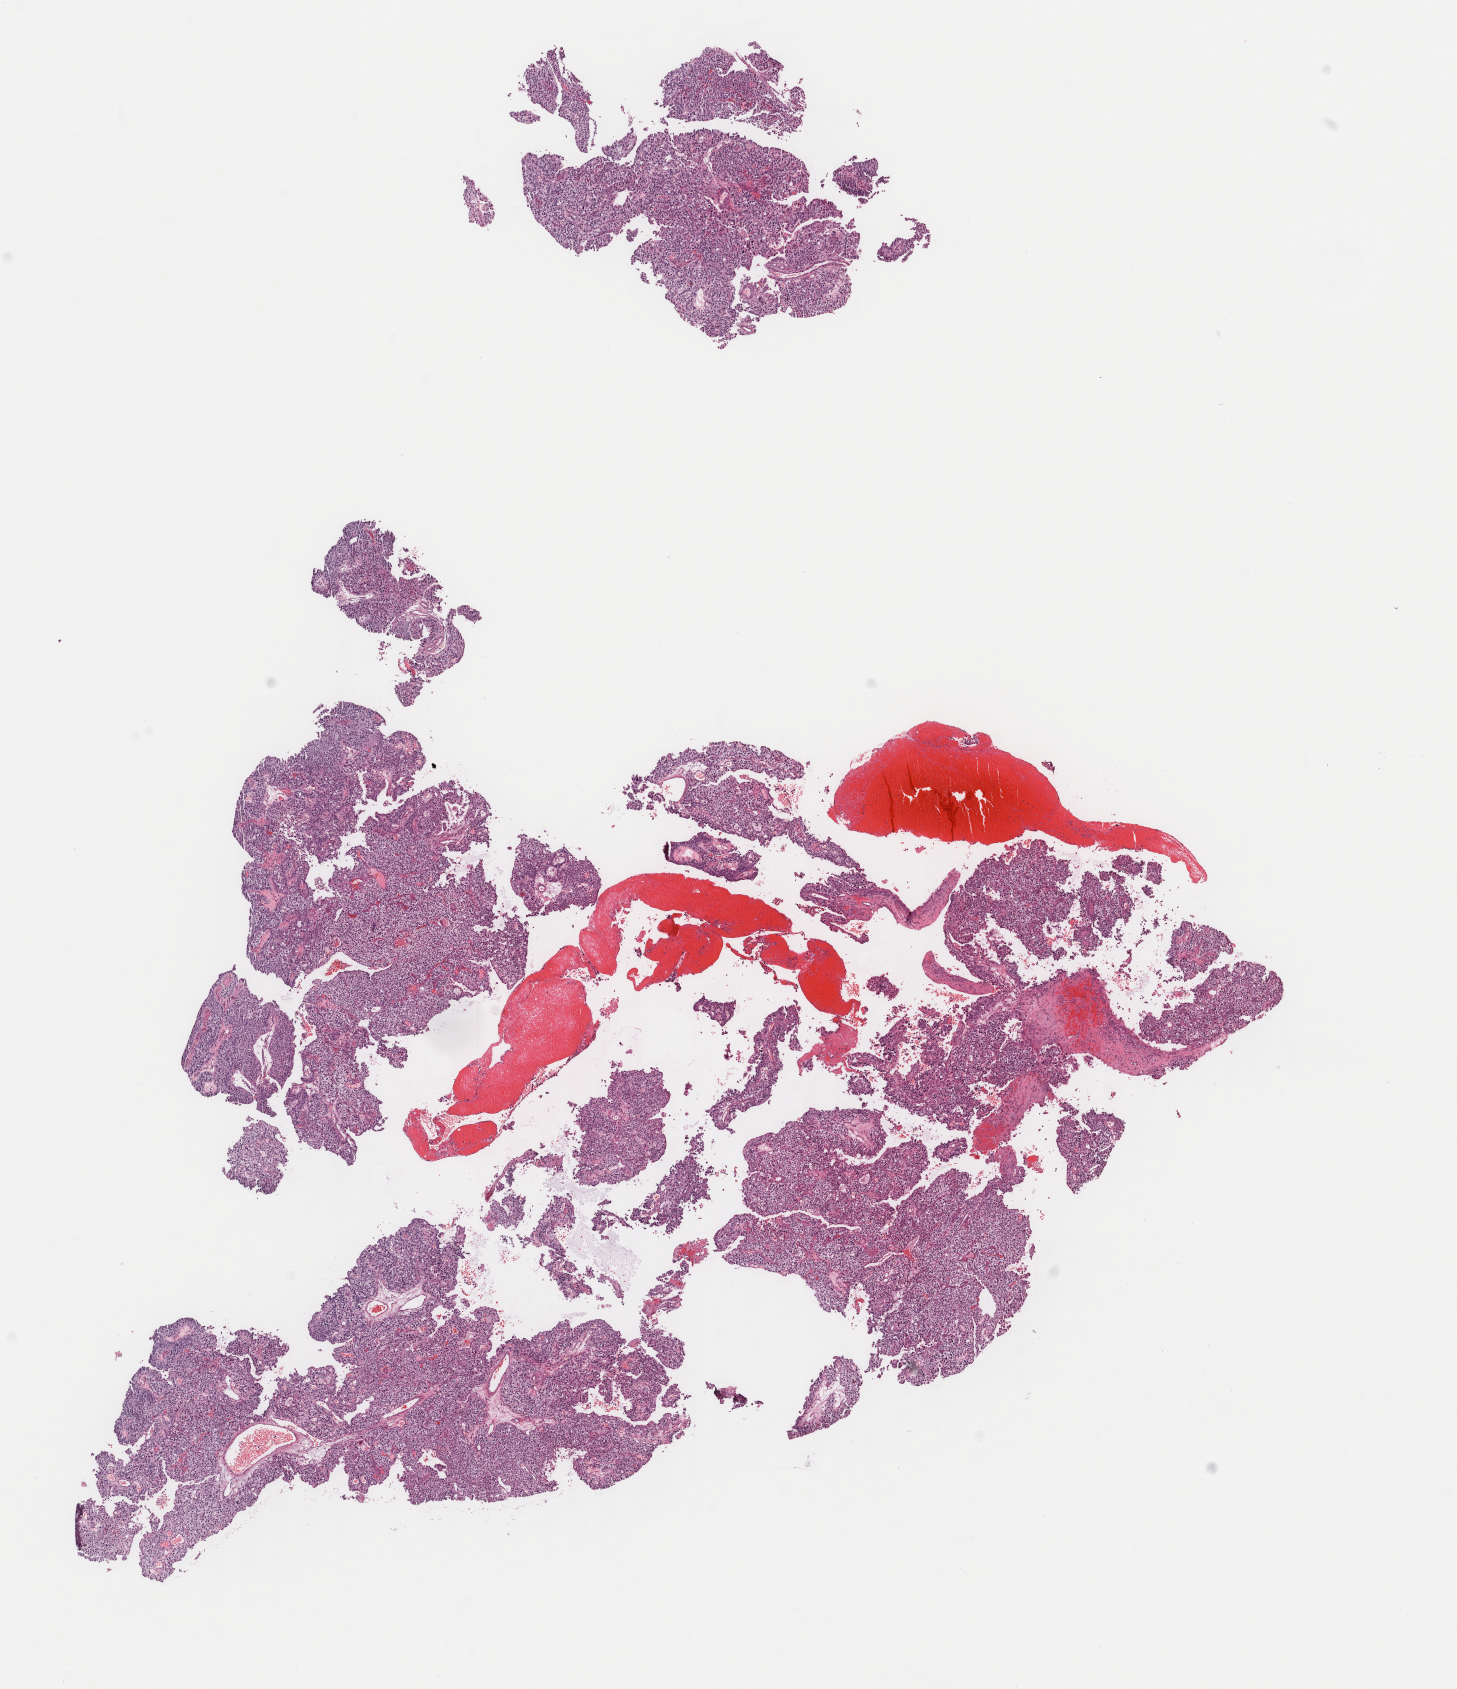
Whole-slide histology image, Hematoxylin and eosin (H&E) stained, a low-resolution overview of the entire scanned area, about 11.6 x 13.4 mm (slide scanned at 40x); frozen section; primary tumour sample from the bladder. Male patient; age at initial diagnosis 73 years. Composition of this section per pathologist review: tumour cells 80%, tumour nuclei 95%, normal cells 0%, stromal cells 20%, necrosis 0%. Inflammatory infiltration, as recorded: lymphocyte infiltration 0%, monocyte infiltration 0%, neutrophil infiltration 0%.
AJCC pathologic stage: I. Pathologic diagnosis: Transitional cell carcinoma (dome of bladder).